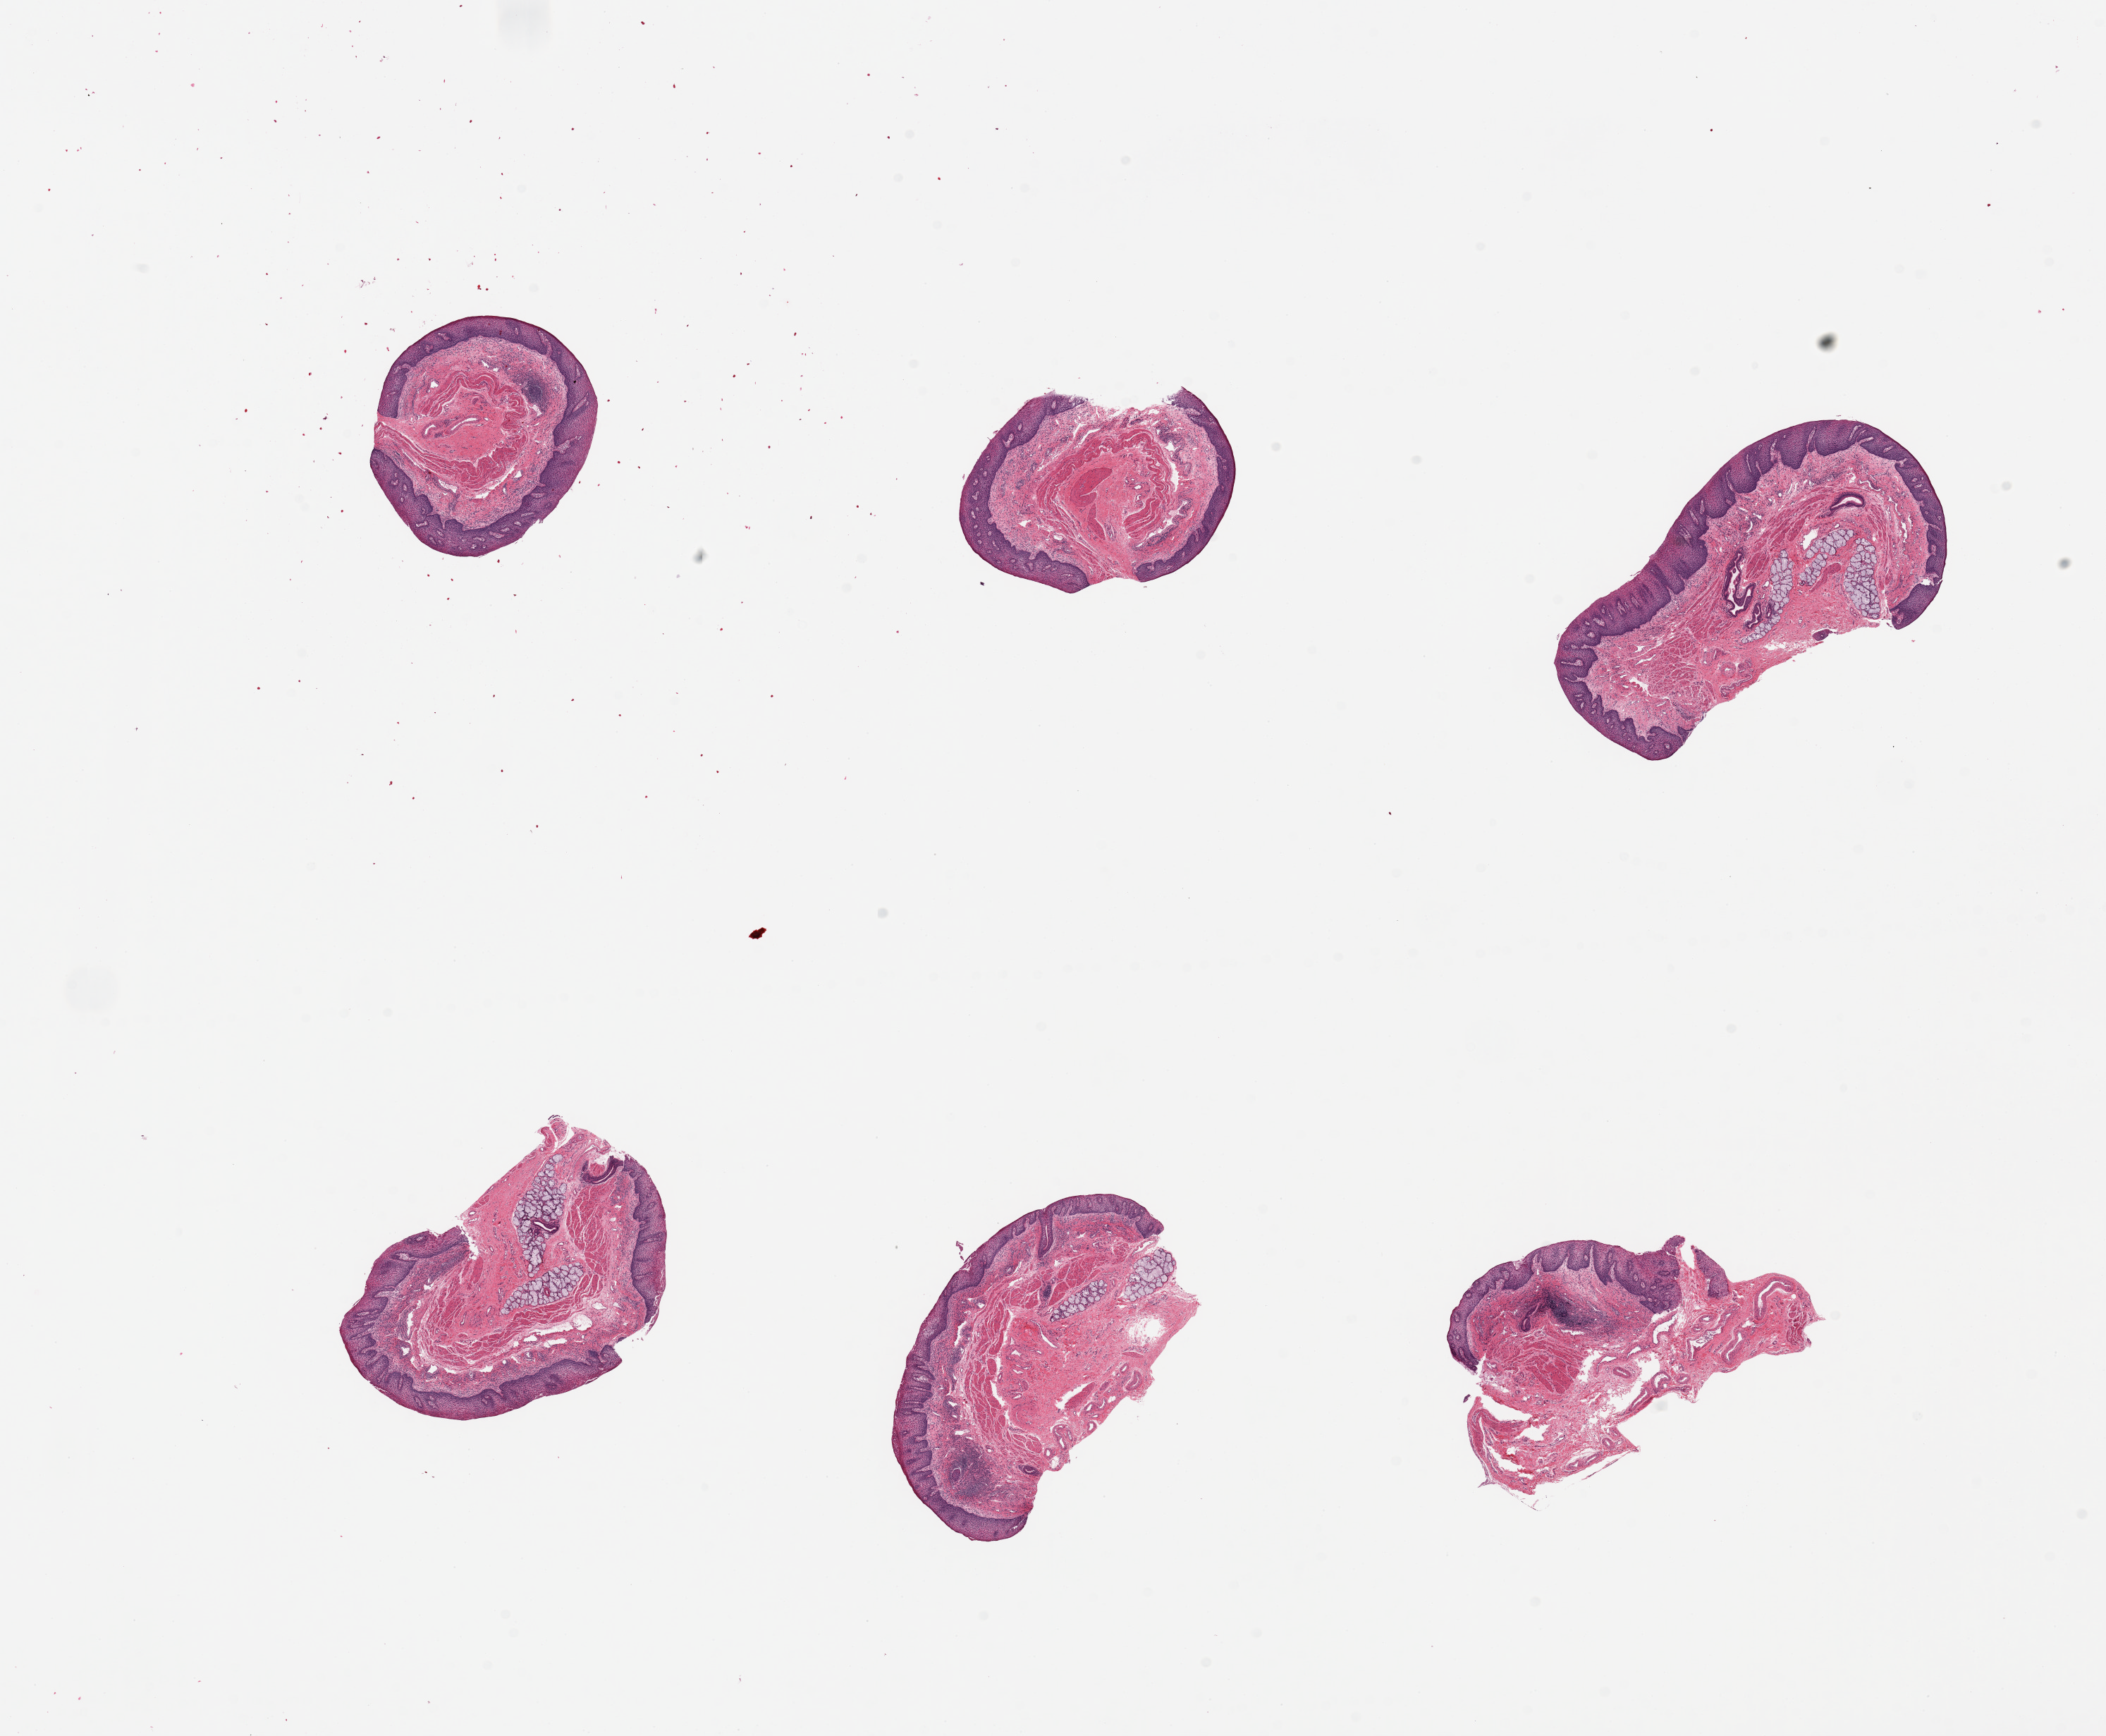
Whole-slide image, H&E stain — shown as a low-resolution overview of the whole scanned area (about 23.6 x 19.5 mm), PAXgene-fixed, paraffin-embedded tissue, target tissue: esophageal mucous membrane, donor tissue sample.
Reviewer comment on this tissue sample: 6 pieces, squamous mucosa well preserved, ~20-25% thickness; Incidental mucous glands present.